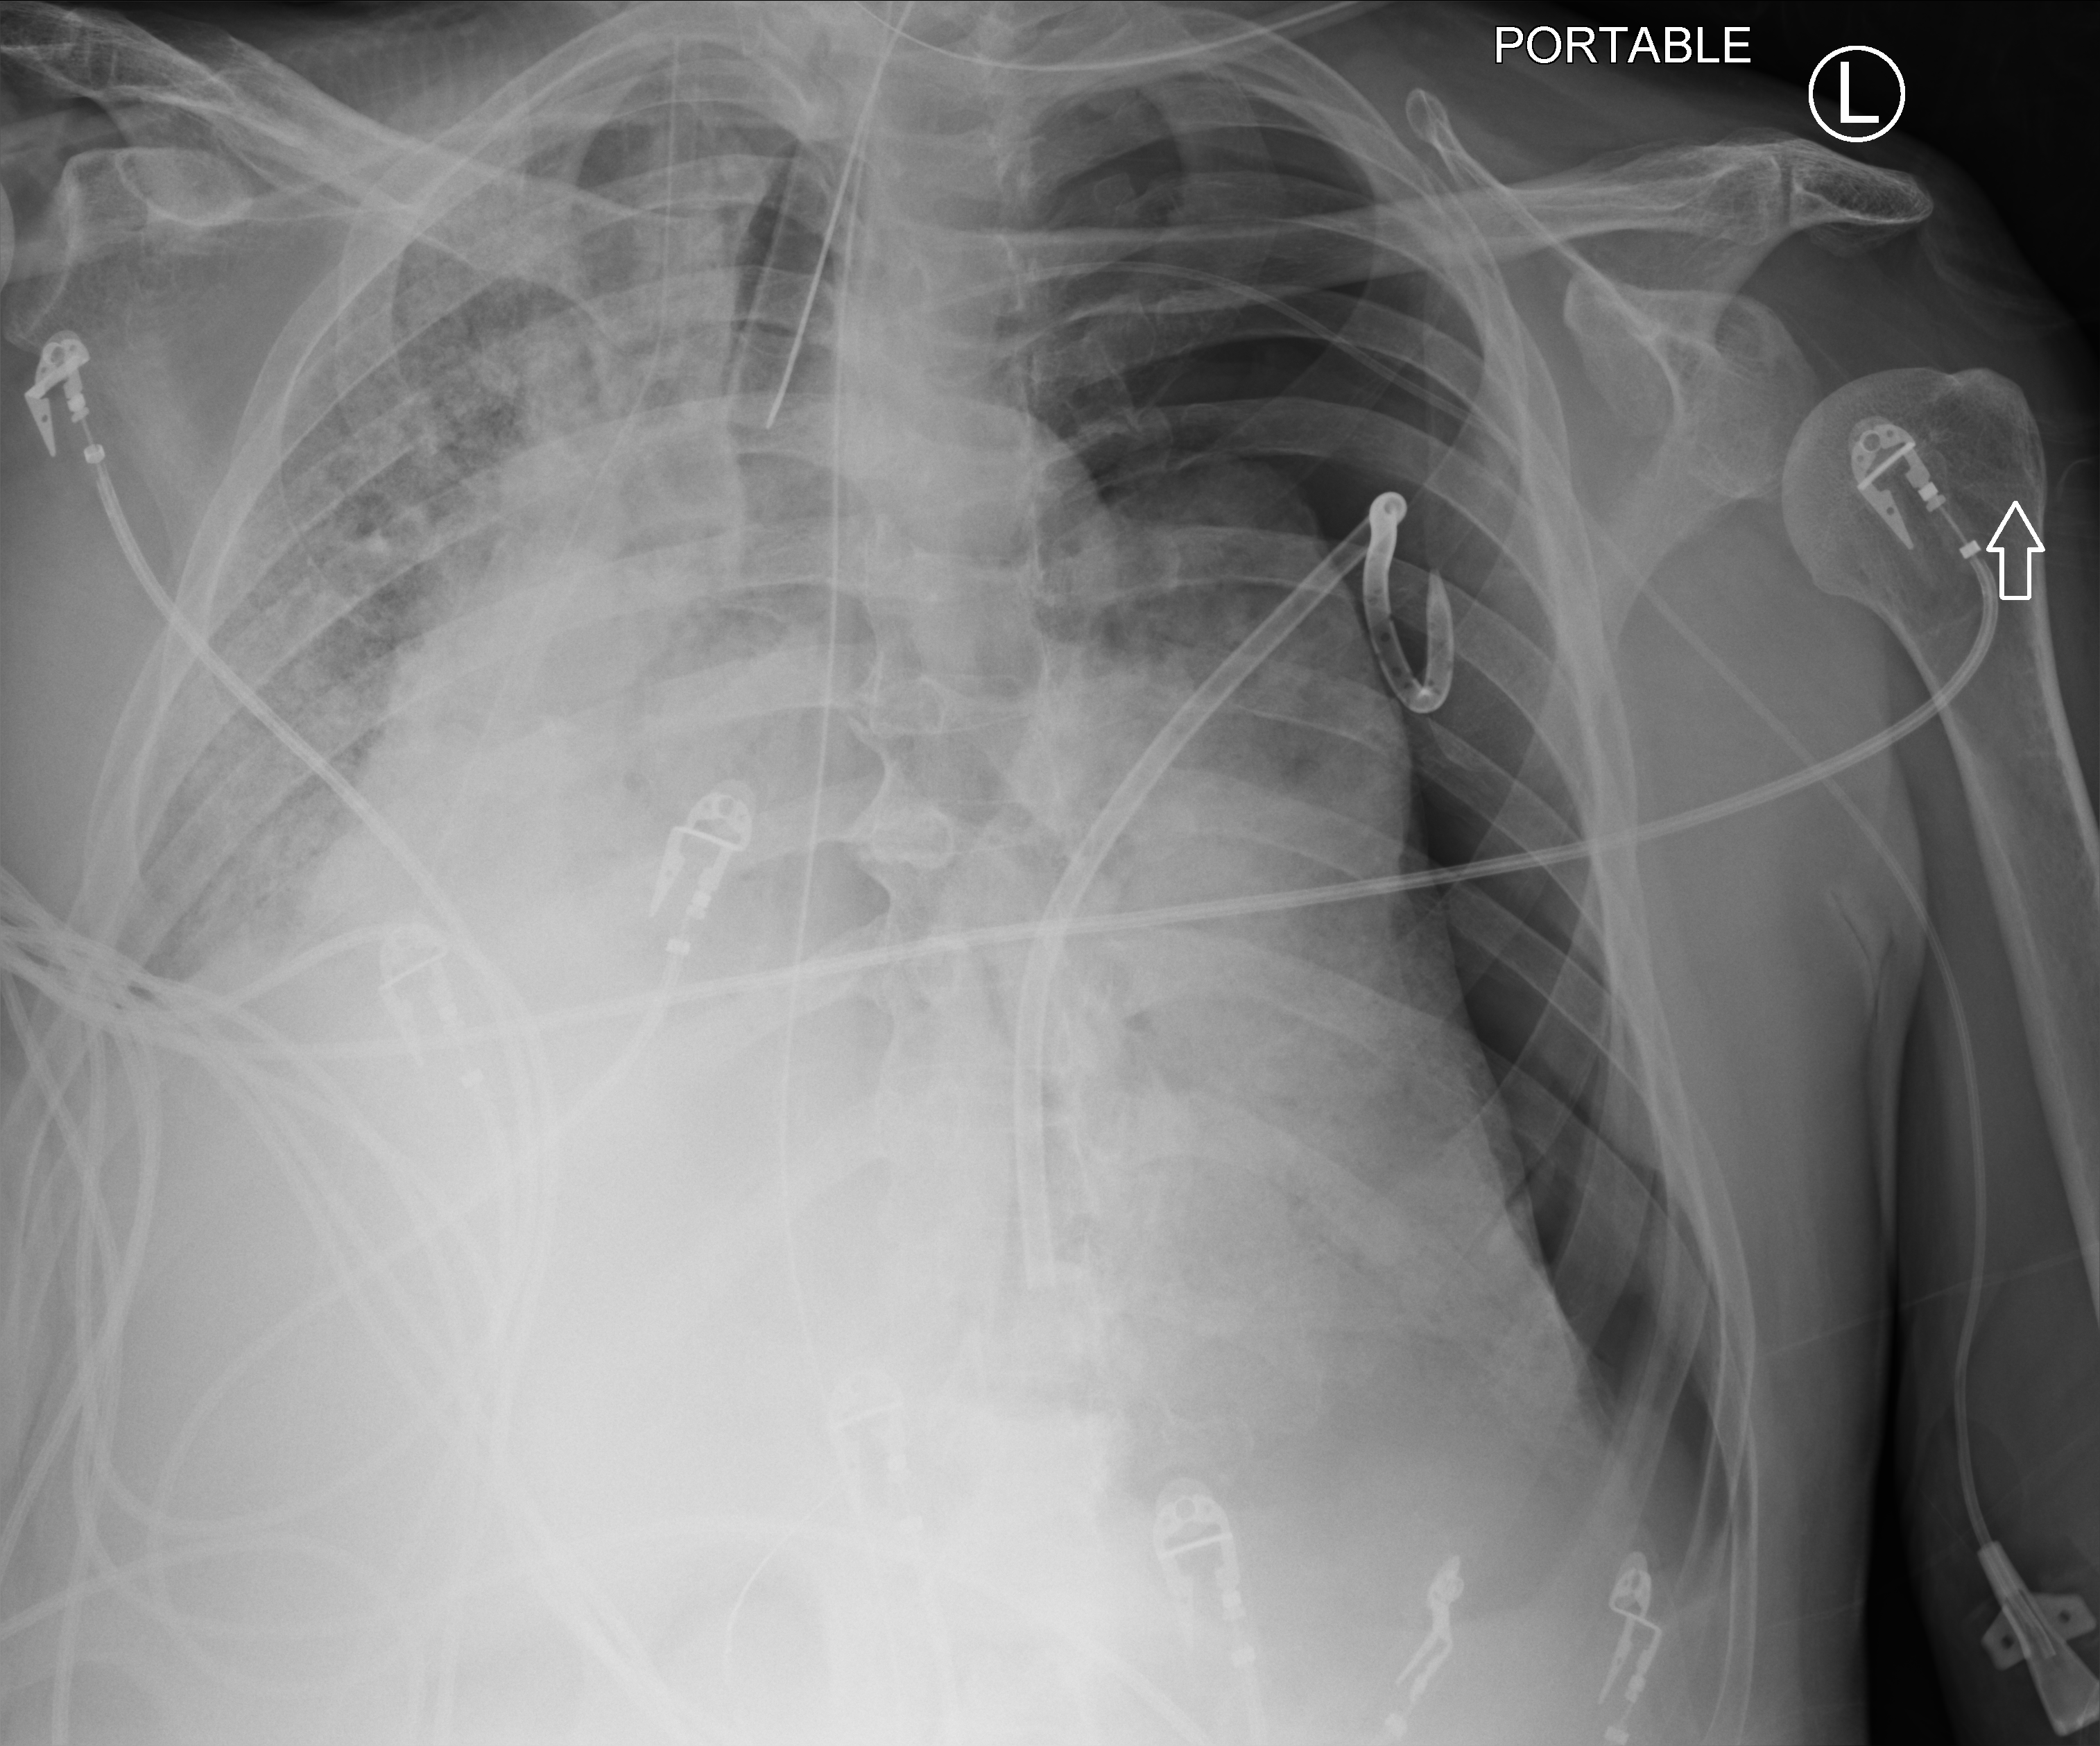
Chest X-ray (portable); anteroposterior (AP) projection. Male patient hospitalised with COVID-19, age 60–74 years.
Admission-level facts for this patient (not findings on this image; timing relative to this image not recorded):
- admitted to intensive care during this hospital stay: yes
- mechanically ventilated during this hospital stay: yes